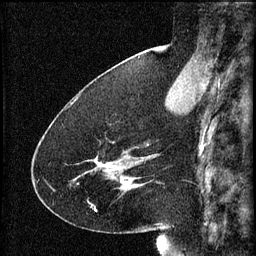
Breast MRI (dynamic contrast-enhanced), one sagittal slice; slice 24 of 60 in the series (ordered by position); 3 images stored at this slice position (order not interpretable as contrast timing); 1.5 T; TE 4.2 ms, TR 8.2 ms; 2 mm slice thickness; 256 × 256 image matrix. Female patient, age 41 years.
Annotated regions visible in this slice (semi-automatic segmentation, software-assisted and operator-edited):
- analysis volume of interest (the breast-tissue region the enhancement analysis was run in; not a lesion): box from (x=75, y=150) to (x=134, y=195) px
- tumour enhancement mask (voxels above the 70 % enhancement threshold inside the analysis volume of interest): (x=95, y=156)–(x=133, y=189)